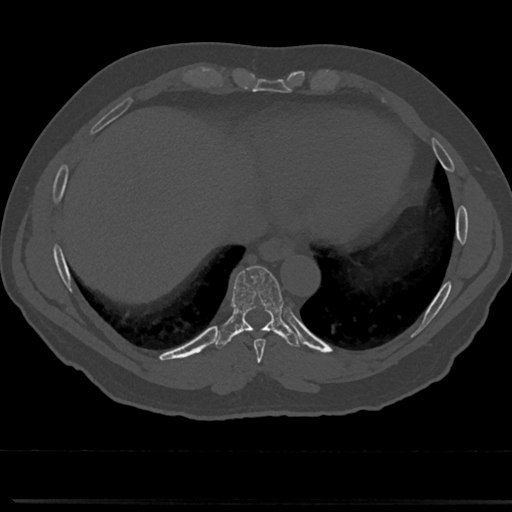
CT including the spine, one axial slice. Position 318 of 817 along the scan axis. Reconstruction kernel Br40s/3. 120 kVp. Bone window (W 1800 / L 400 HU). 512 × 512 image matrix. Male patient, age 61 years. Case-level facts recorded for this patient, not image findings: primary cancer: prostate.
Annotated regions visible in this slice (semi-automatic segmentation, software-assisted and operator-edited):
- T7 vertebra: box from (x=258, y=363) to (x=266, y=376) px
- T8 vertebra: (x=218, y=267)–(x=305, y=356)